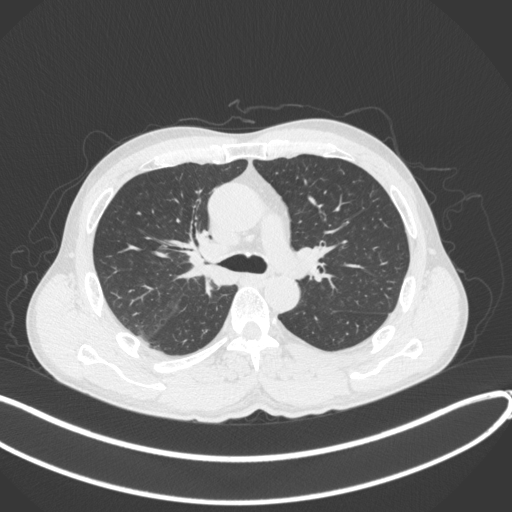
Chest CT, one axial slice; reconstruction kernel B31f; 120 kVp; lung window (W 1500 / L -600 HU); 1 mm slice thickness; 512 × 512 image matrix, field of view 400 × 400 mm. Patient: male, 53 years. From the clinical record (not read from this slice): clinical TNM (as recorded): T1b N0 M0.
Outlined on this slice (bounding box drawn by a radiologist):
- lung tumour (recorded histology: squamous cell carcinoma): box from (x=183, y=233) to (x=233, y=292) px